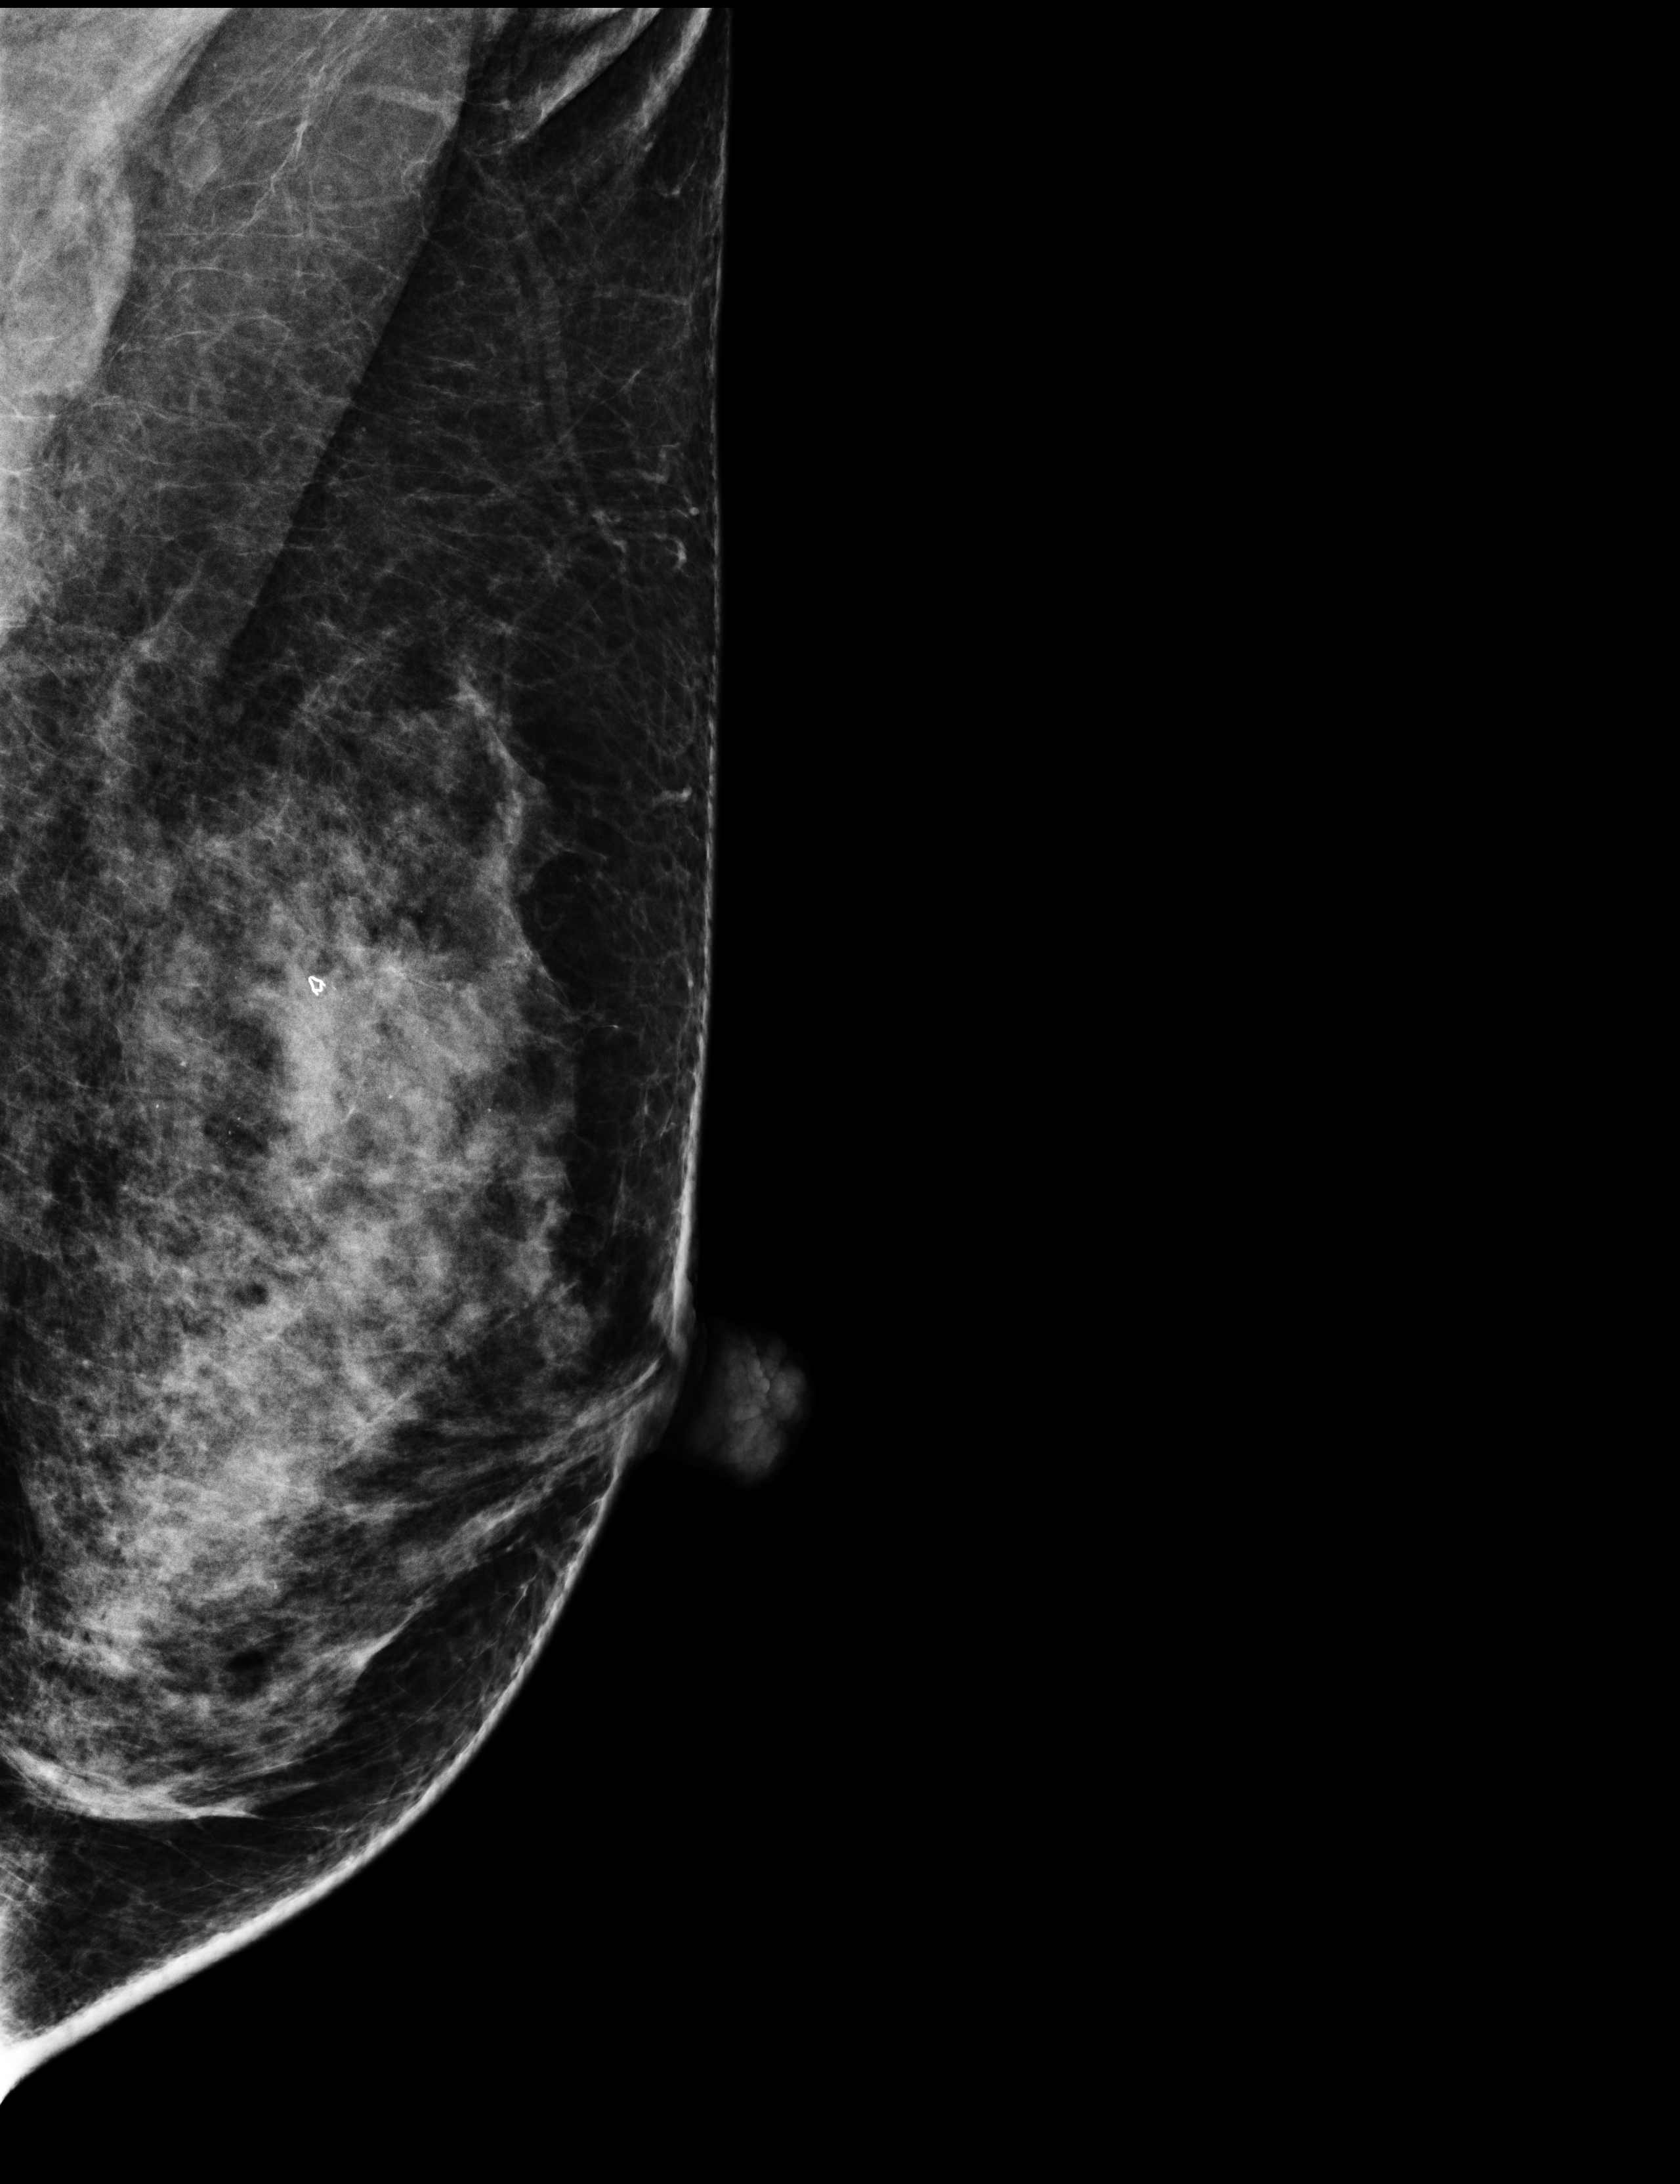
Digital mammogram (FFDM), left breast, mediolateral oblique (MLO) view, annual screening mammography examination, compressed breast thickness 67 mm. Female patient, age 53 years.
BI-RADS breast density category at the screening exam (both breasts, scale 1–4): 4. Final BI-RADS category for the screening round (tomosynthesis exam, both breasts): category 2. Recall: no recall after this screen.